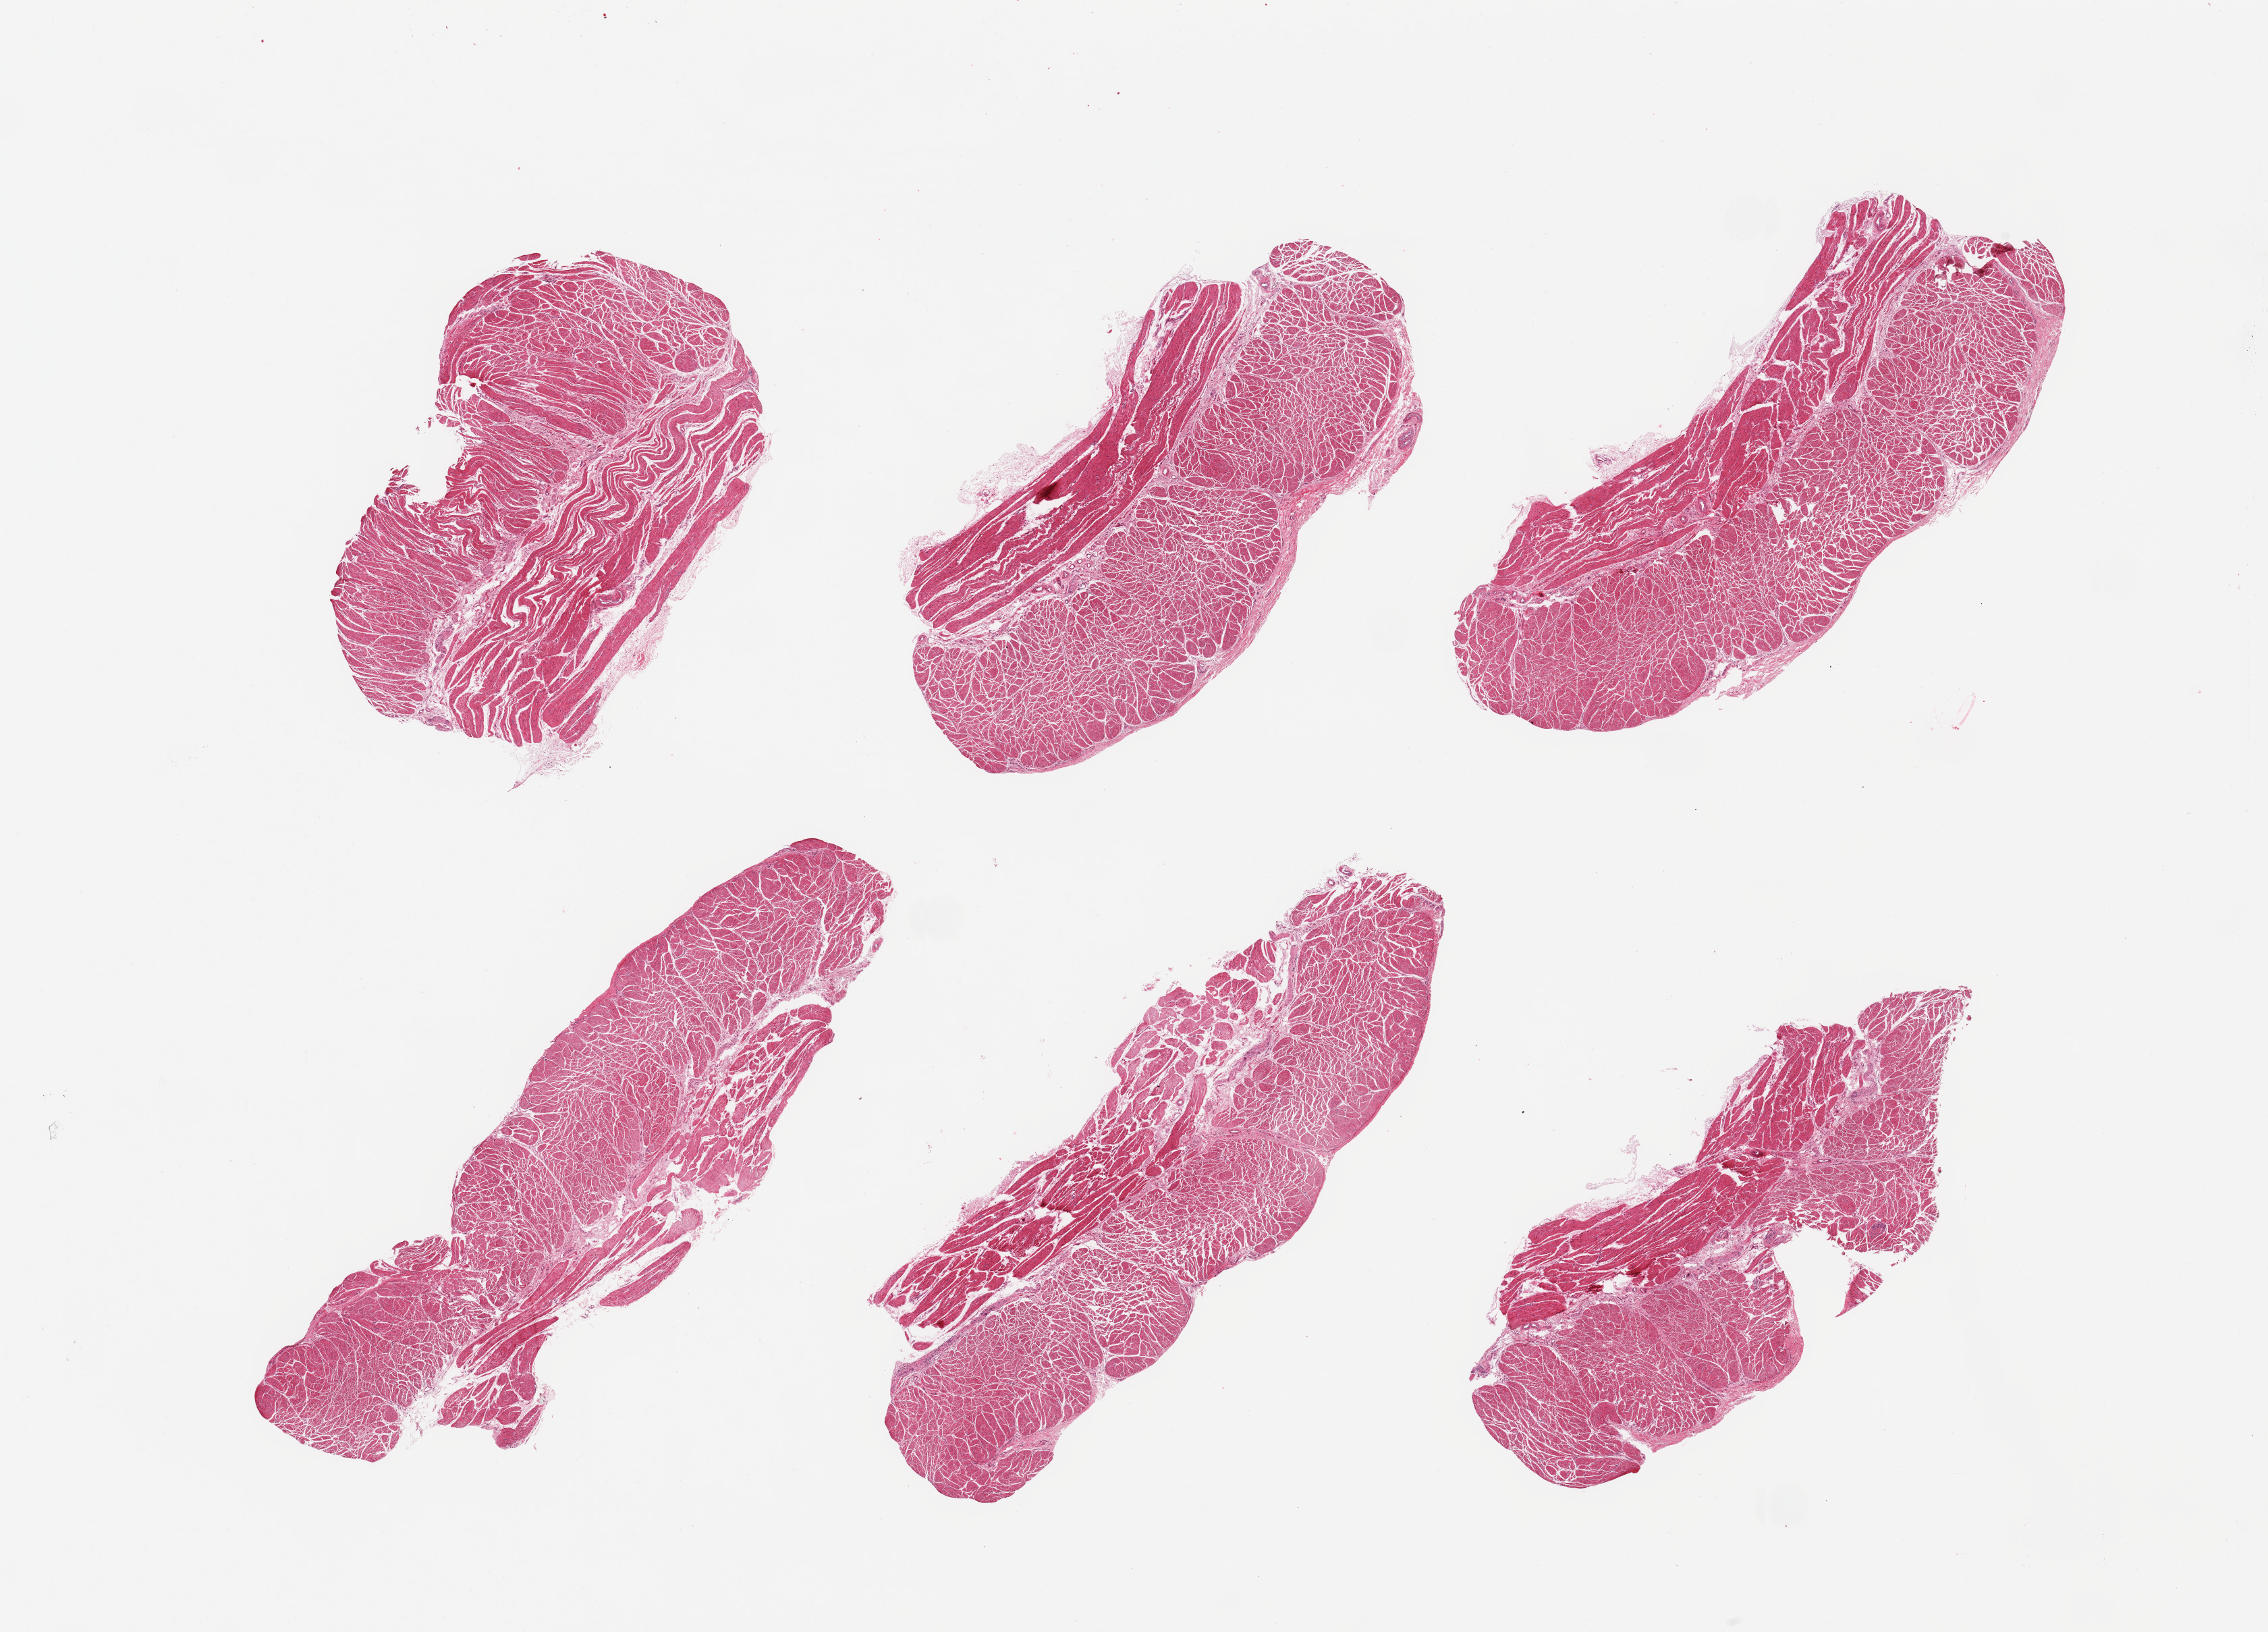
Digitized hematoxylin and eosin (H&E)-stained section — low-resolution overview of the scanned area, about 26.6 x 19.1 mm; PAXgene-fixed, paraffin-embedded tissue; section of esophageal muscle (target tissue); donor tissue sample. Donor sex: female.
* pathologist's review note for this sample: 6 pieces; target muscularis